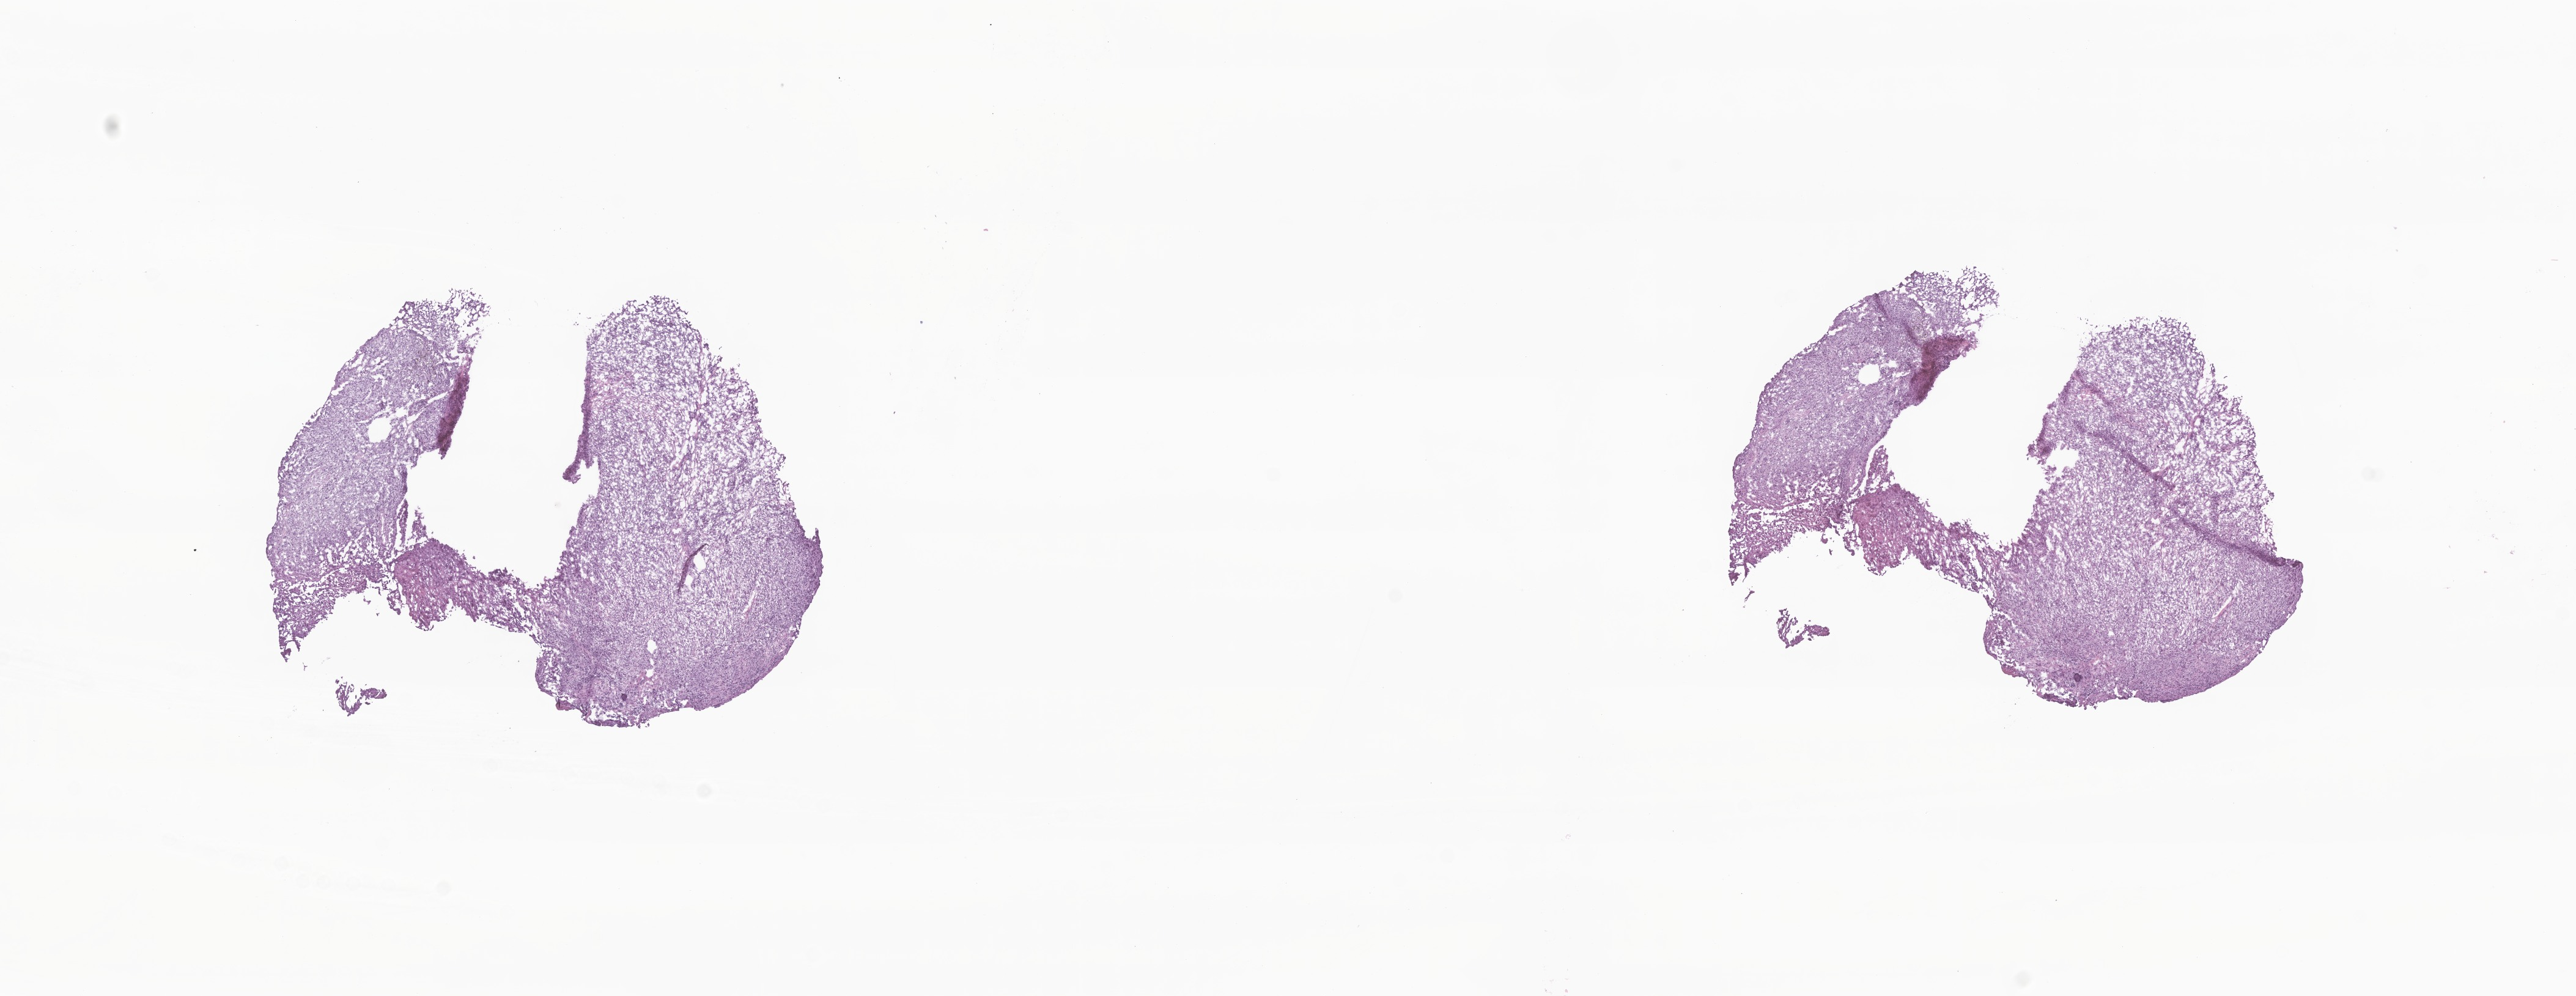
Digitized H&E-stained section, low-resolution overview of the scanned area, about 17.8 x 6.9 mm. Frozen section (tissue freezing medium). Specimen: metastatic tumor tissue, resected from brain. Patient: female, age at initial diagnosis 59 years. Composition of this section per pathologist review: tumor cells 90%, tumor nuclei 90%, stromal cells 10%, necrosis 0%, normal cells 0%. Inflammatory infiltration, as recorded: lymphocyte infiltration 0%, monocyte infiltration 0%, neutrophil infiltration 0%.
Patient diagnosis (primary): Malignant melanoma, NOS.